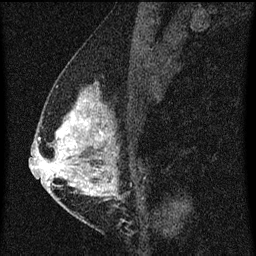
Breast MRI (dynamic contrast-enhanced), one sagittal slice; slice 28 of 60 in the series (ordered by position); dynamic contrast-enhanced series, image 2 of 3 at this slice position (ordered by acquisition); 1.5 T; TE 4.2 ms, TR 8 ms; 2 mm slice thickness; 256 × 256 image matrix, field of view 180 × 180 mm. Female patient, age 47 years.
Structures marked on this image (semi-automatically segmented with operator editing):
- analysis volume of interest (the breast-tissue region the enhancement analysis was run in; not a lesion): box from (x=50, y=80) to (x=138, y=203) px
- tumour enhancement mask (voxels above the 70 % enhancement threshold inside the analysis volume of interest): (x=50, y=100)–(x=115, y=201)